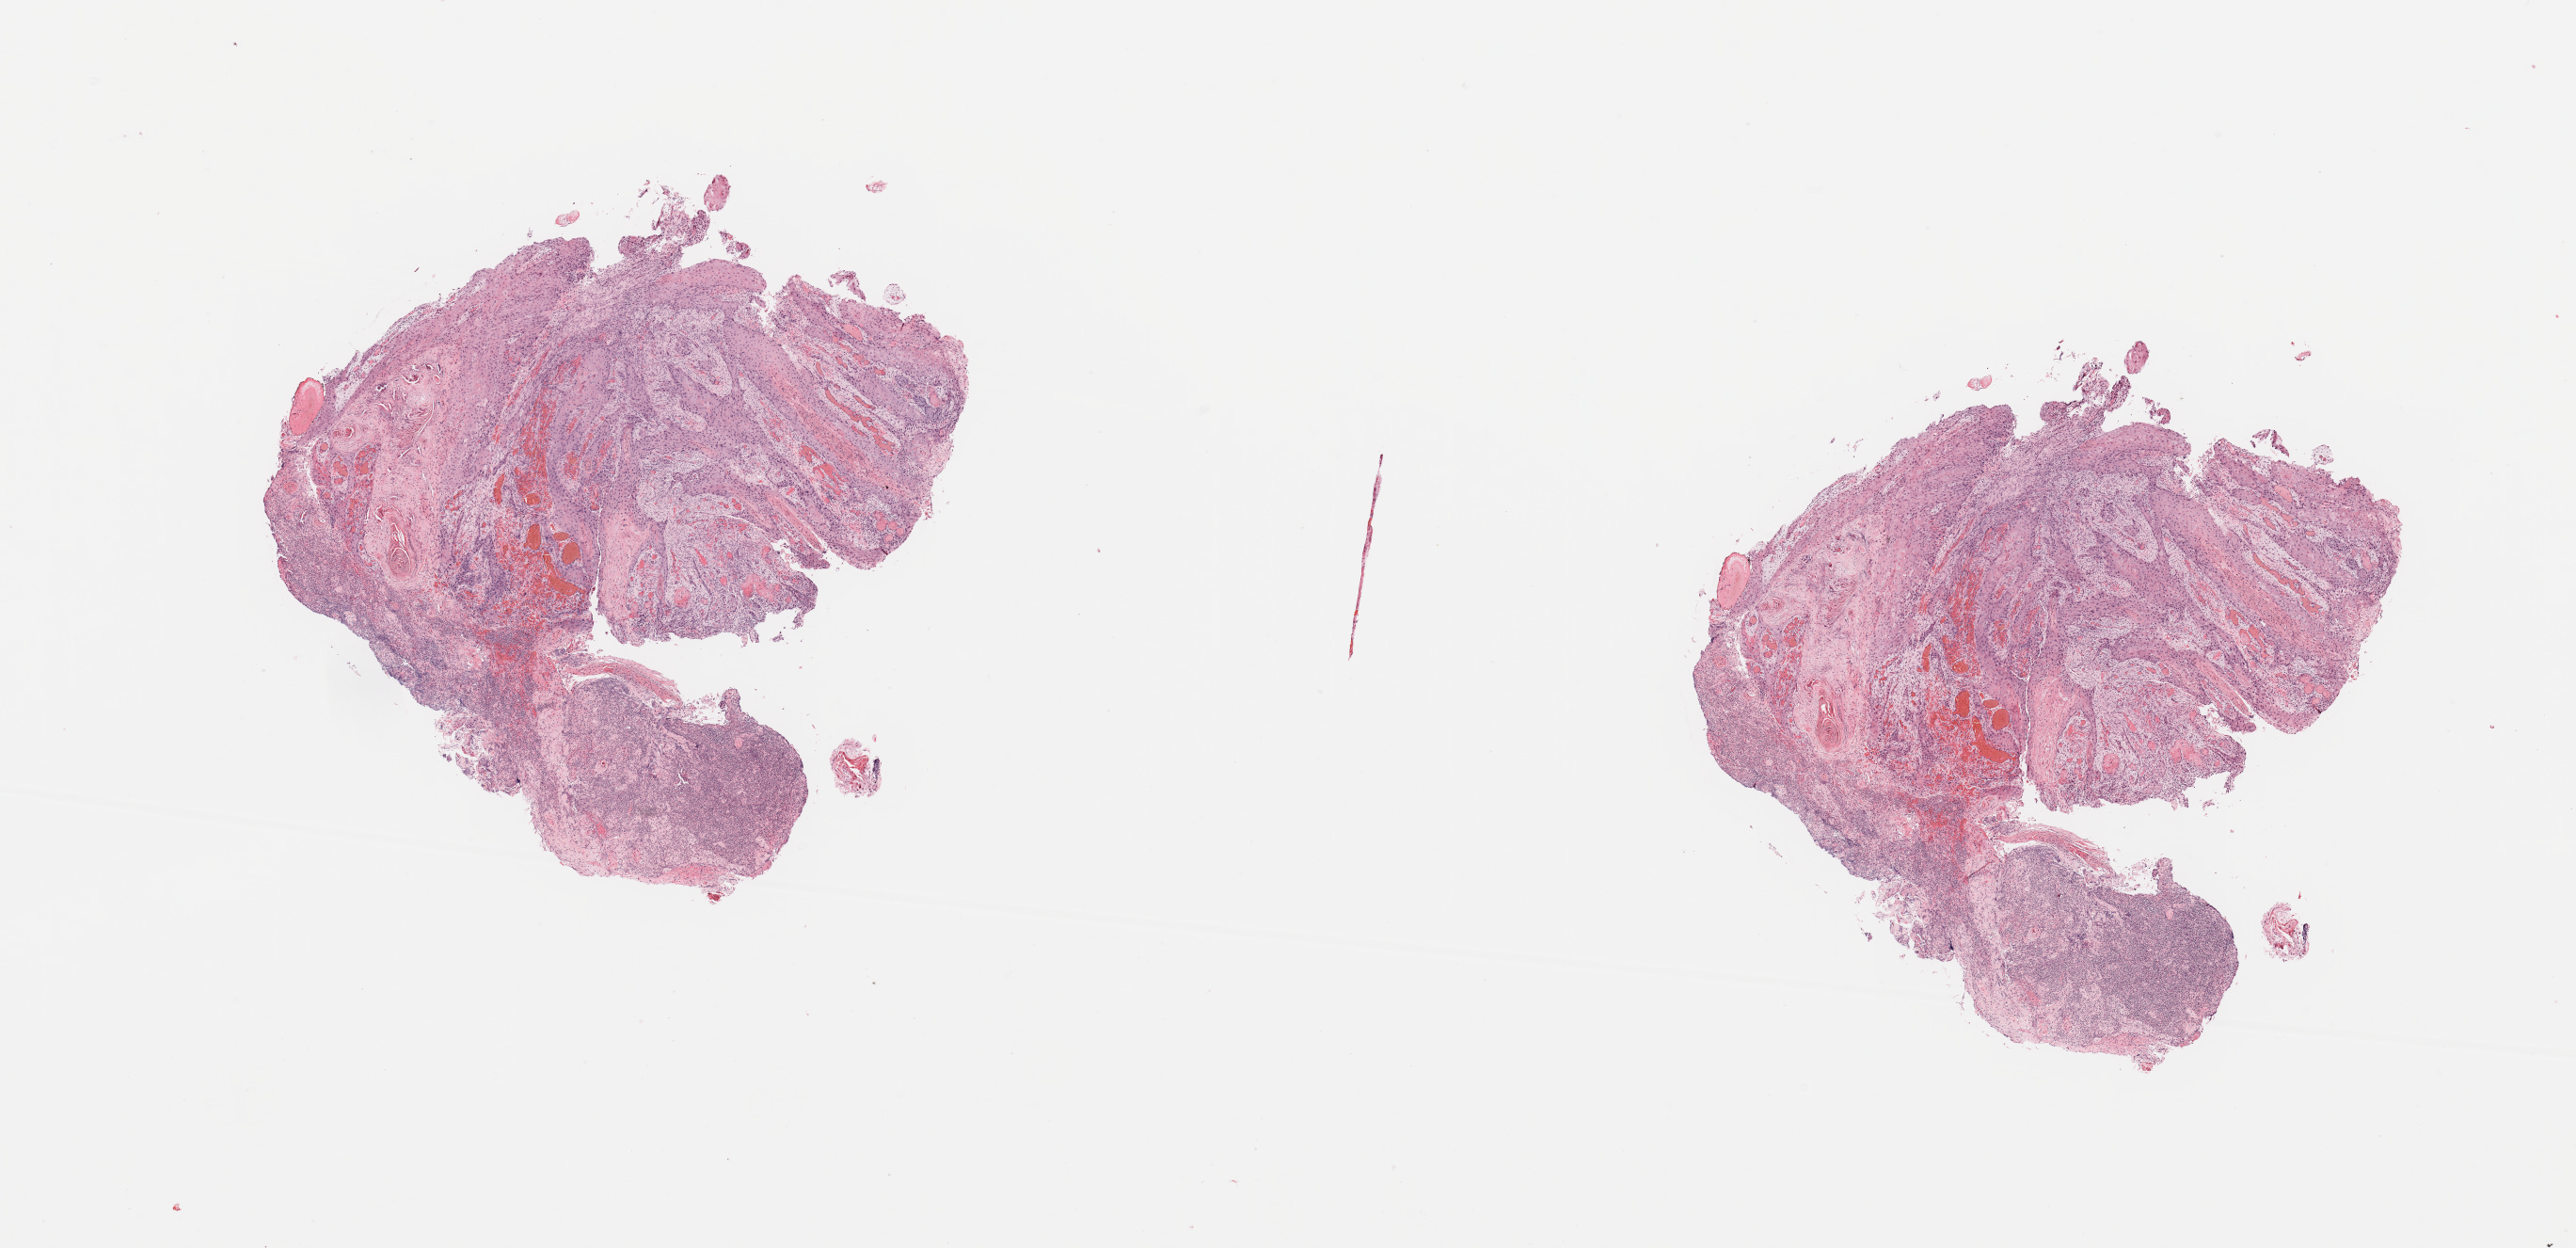
Digitized H&E tissue section (whole slide) — a low-resolution overview of the entire scanned area, about 21.7 x 10.5 mm (acquisition: 20x scan). Head and neck, tissue type not recorded. Female, 67 y/o.
Patient diagnosis: Squamous cell carcinoma, NOS (overlapping lesion of lip, oral cavity and pharynx).